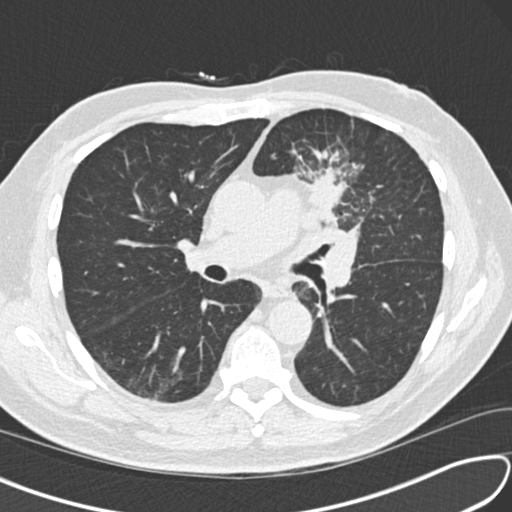
Low-dose screening chest CT, one axial slice. Position 88 of 156 along the scan axis. Reconstruction kernel B30f. 120 kVp. Lung window (W 1500 / L -600 HU). 2 mm slice thickness. 512 × 512 image matrix, field of view 340 × 340 mm.
Structures marked on this image (manually delineated by an expert):
- lesion 1 (tumor, upper lobe of left lung): box from (x=307, y=165) to (x=348, y=230) px